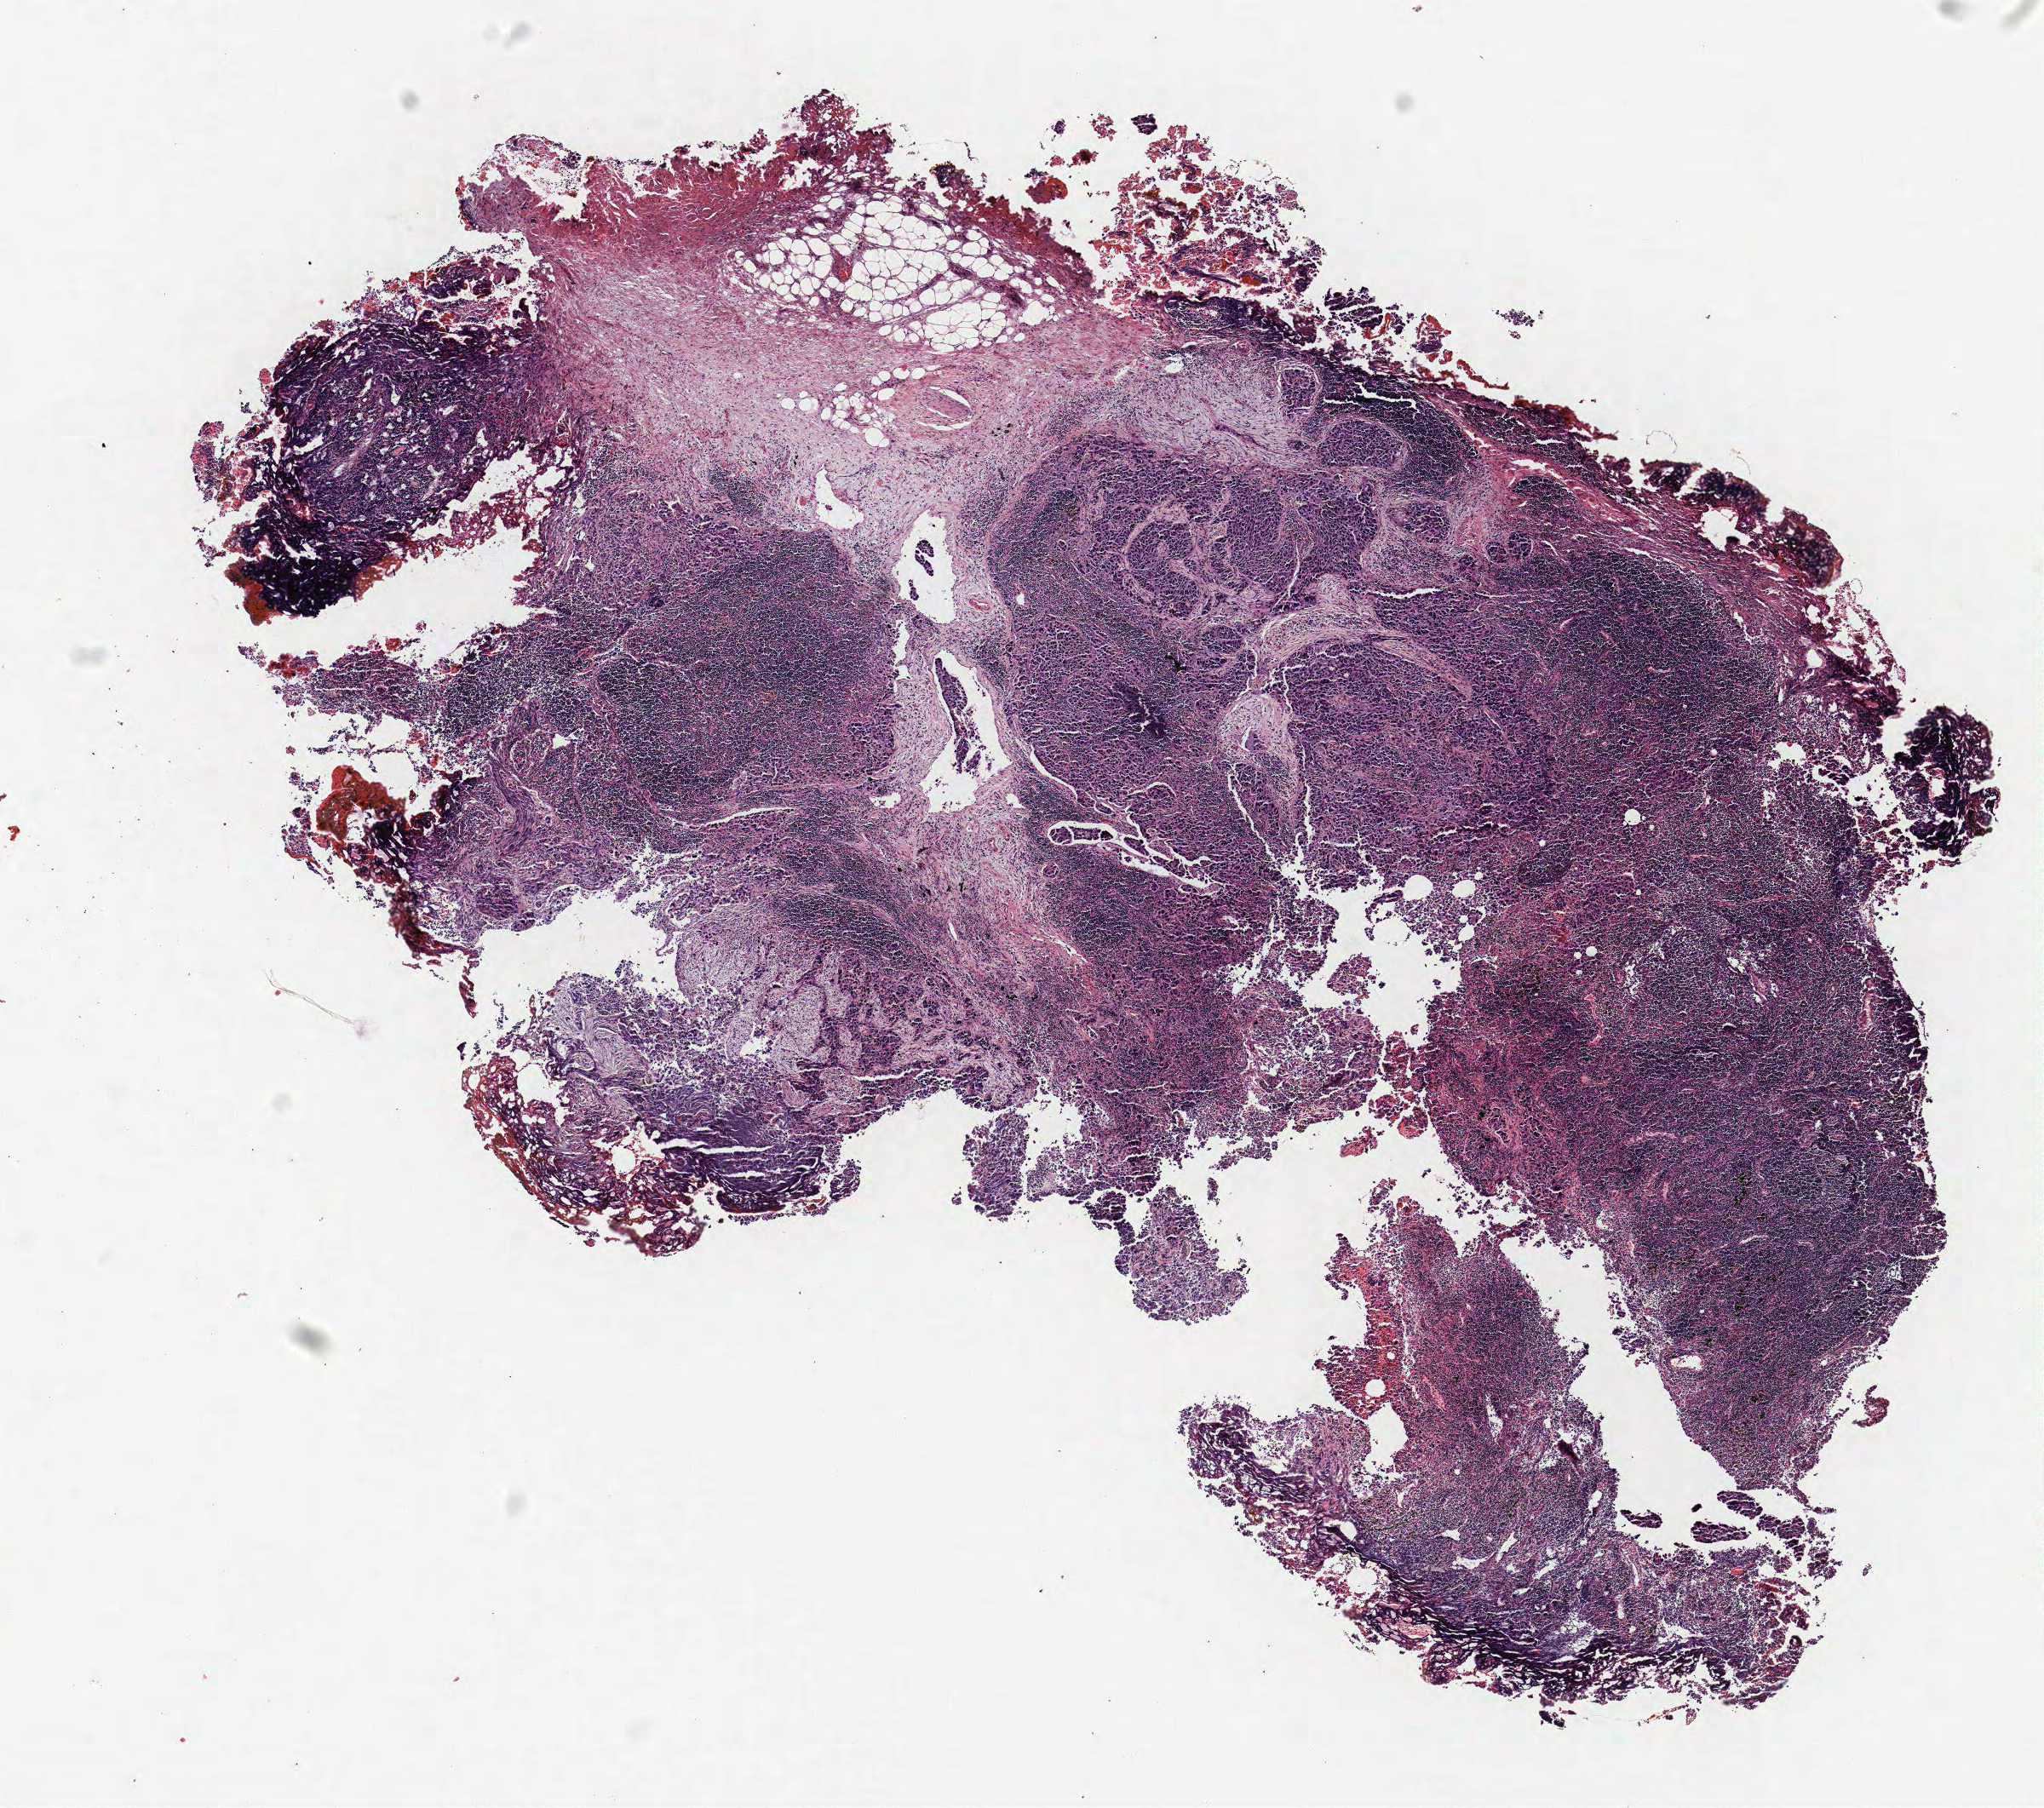
H&E-stained whole-slide image — shown as a low-resolution overview of the whole scanned area (about 9.6 x 8.5 mm). FFPE section. Lung tissue. Male, age 64 at enrolment. Grade: poorly differentiated (G3).
* stage (AJCC 6th edition): IIIA
* tumour size (pathology): 20 mm
* primary tumour location (clinical record): right middle lobe
* participant's lung-cancer diagnosis: Non-small cell carcinoma